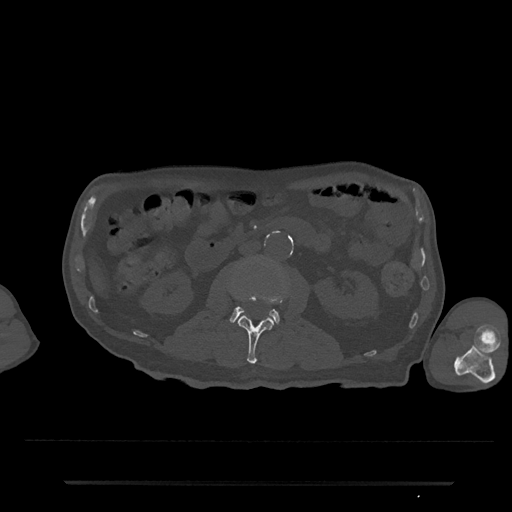
CT including the spine, one axial slice. Position 33 of 797 along the scan axis. Reconstruction kernel Br40s/3. 120 kVp. Bone window (W 1800 / L 400 HU). 0.5 mm slice thickness. 512 × 512 image matrix, field of view 427 × 427 mm. Male patient, age 74 years. From the clinical record (not read from this slice): primary cancer: prostate.
Structures marked on this image (semi-automatic segmentation, software-assisted and operator-edited):
- L2 vertebra: bounding box <238,292,283,364> (left, top, right, bottom; pixels)
- L3 vertebra: <230,306,280,325>